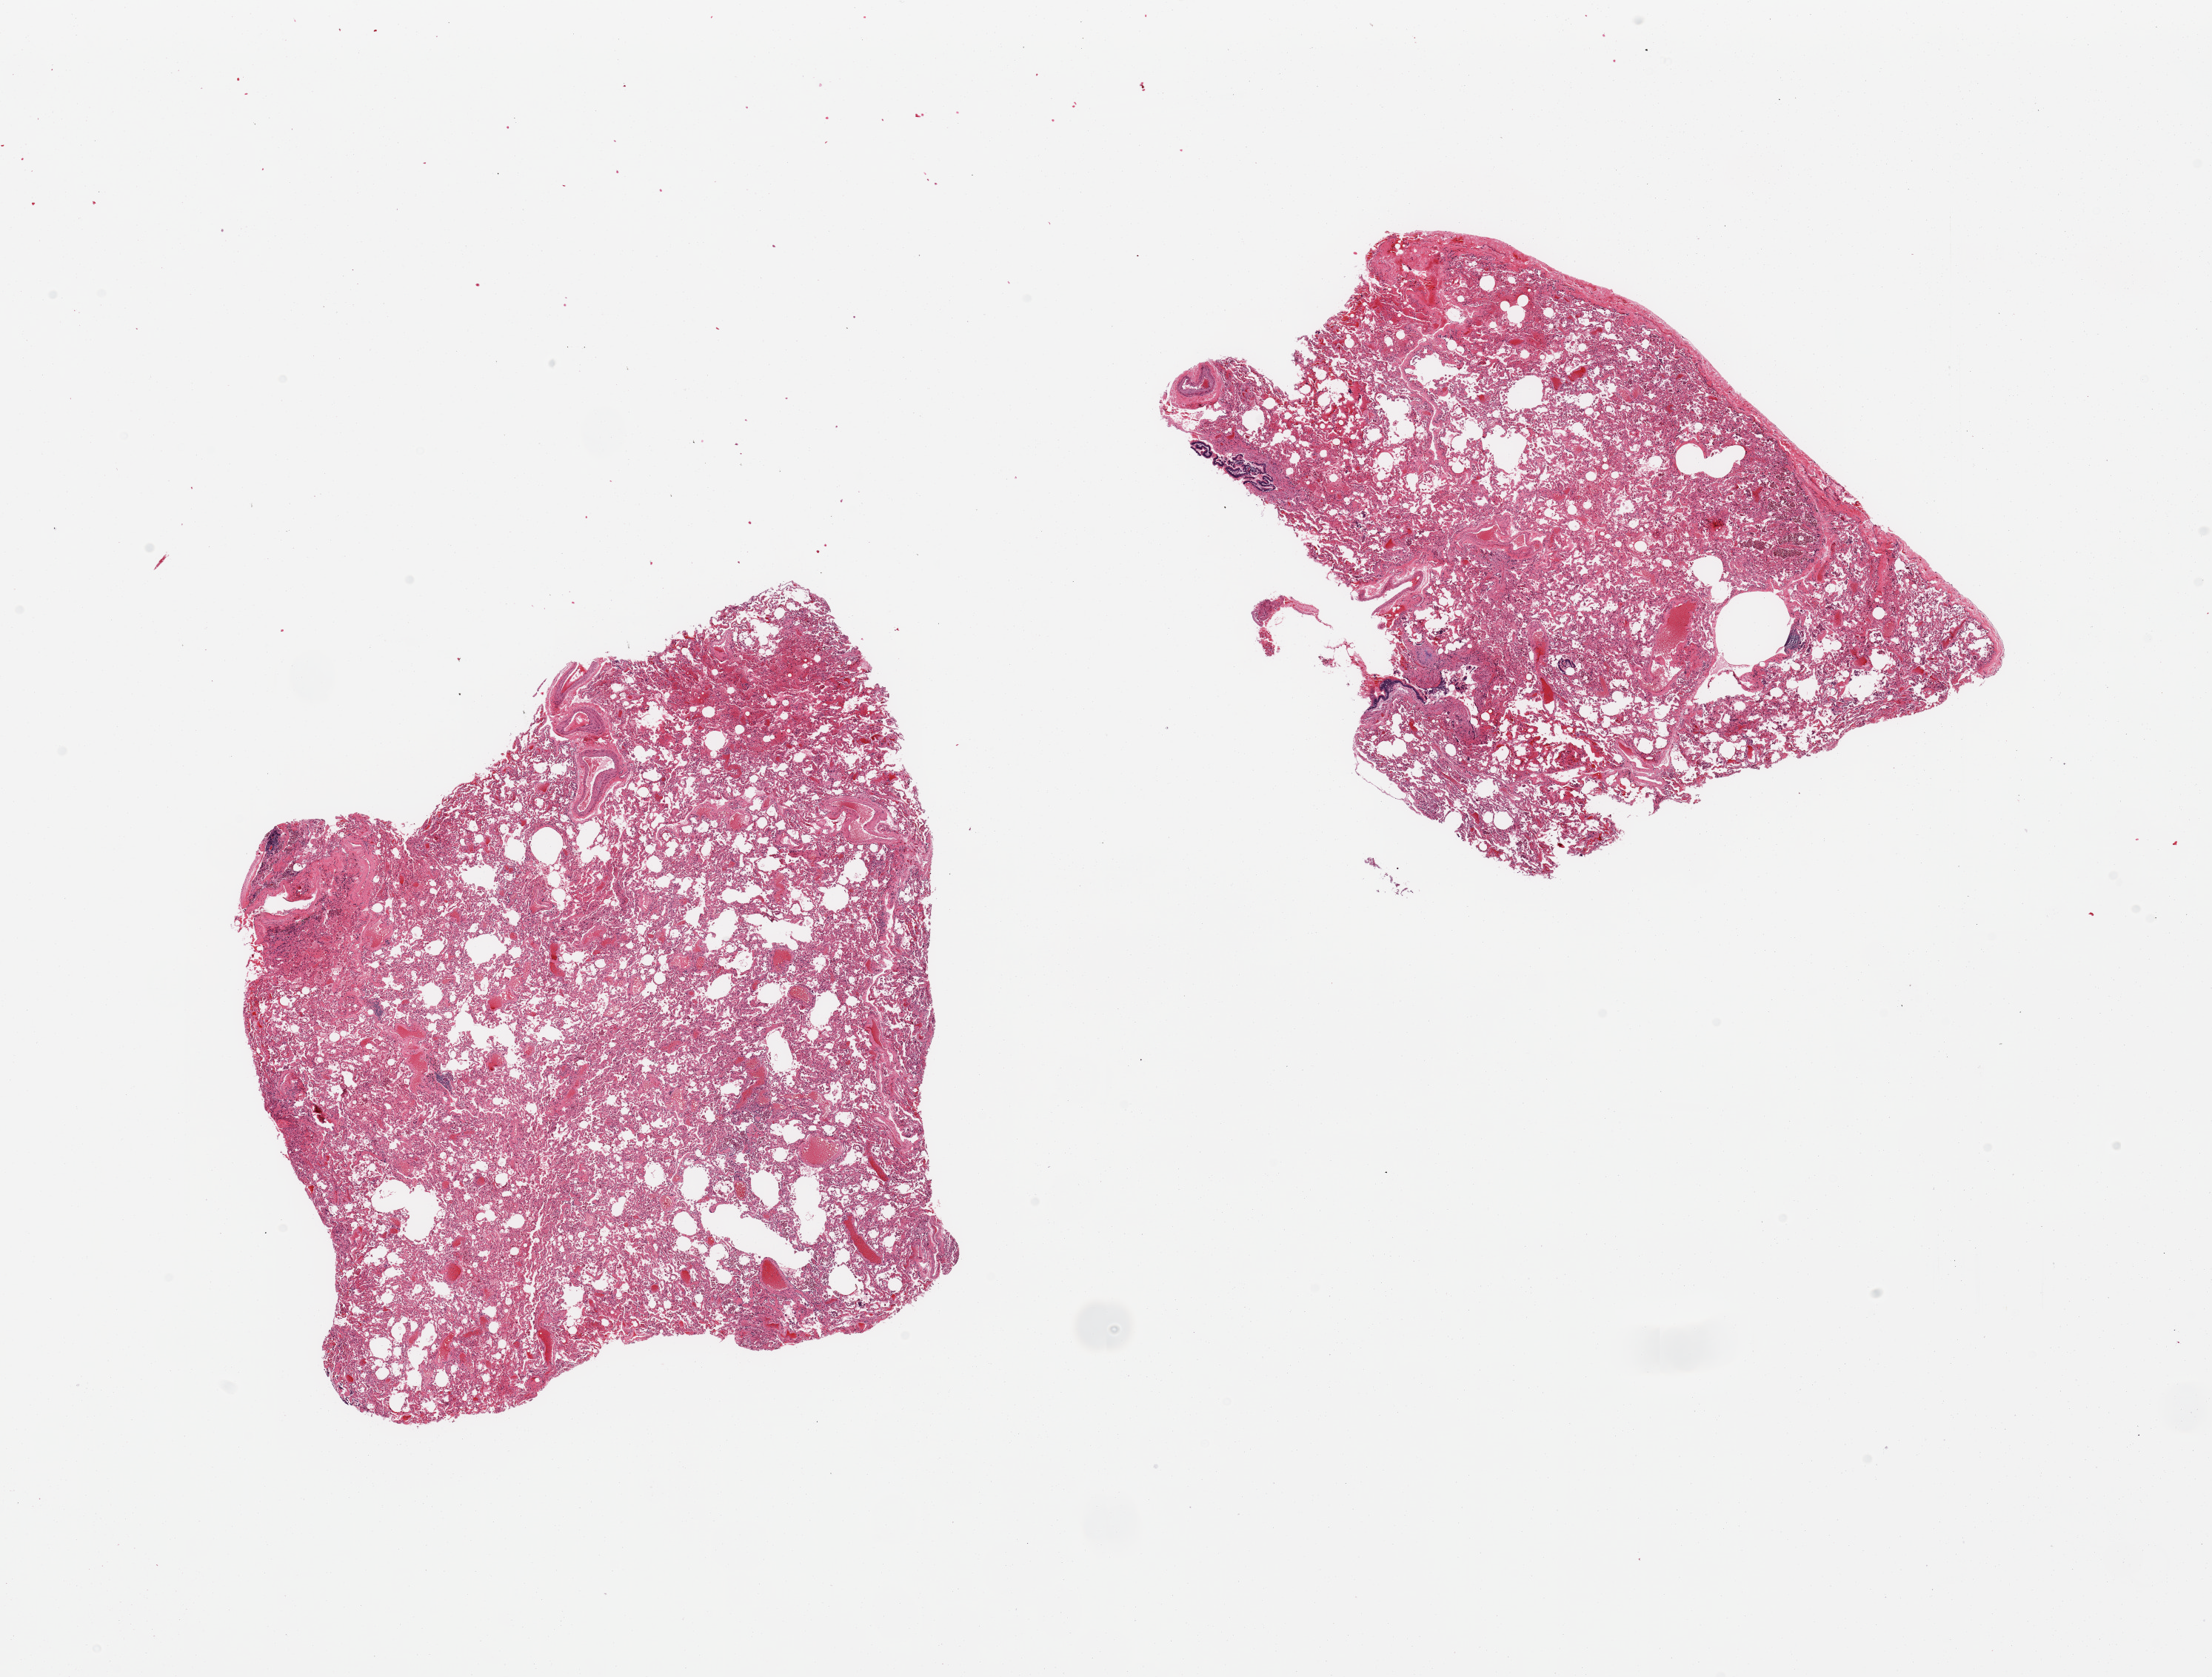
Digitized haematoxylin and eosin-stained section — low-resolution overview of the scanned area, about 23.6 x 17.9 mm (acquisition: 20x scan), PAXgene-fixed paraffin-embedded (PFPE) section, section of lung (target tissue), donor tissue sample. Donor: female.
• reviewer comment on this tissue sample: 2 pieces, some congestion and hemorrhage and many hemosiderin-laden macrophages, small focus of cartilage